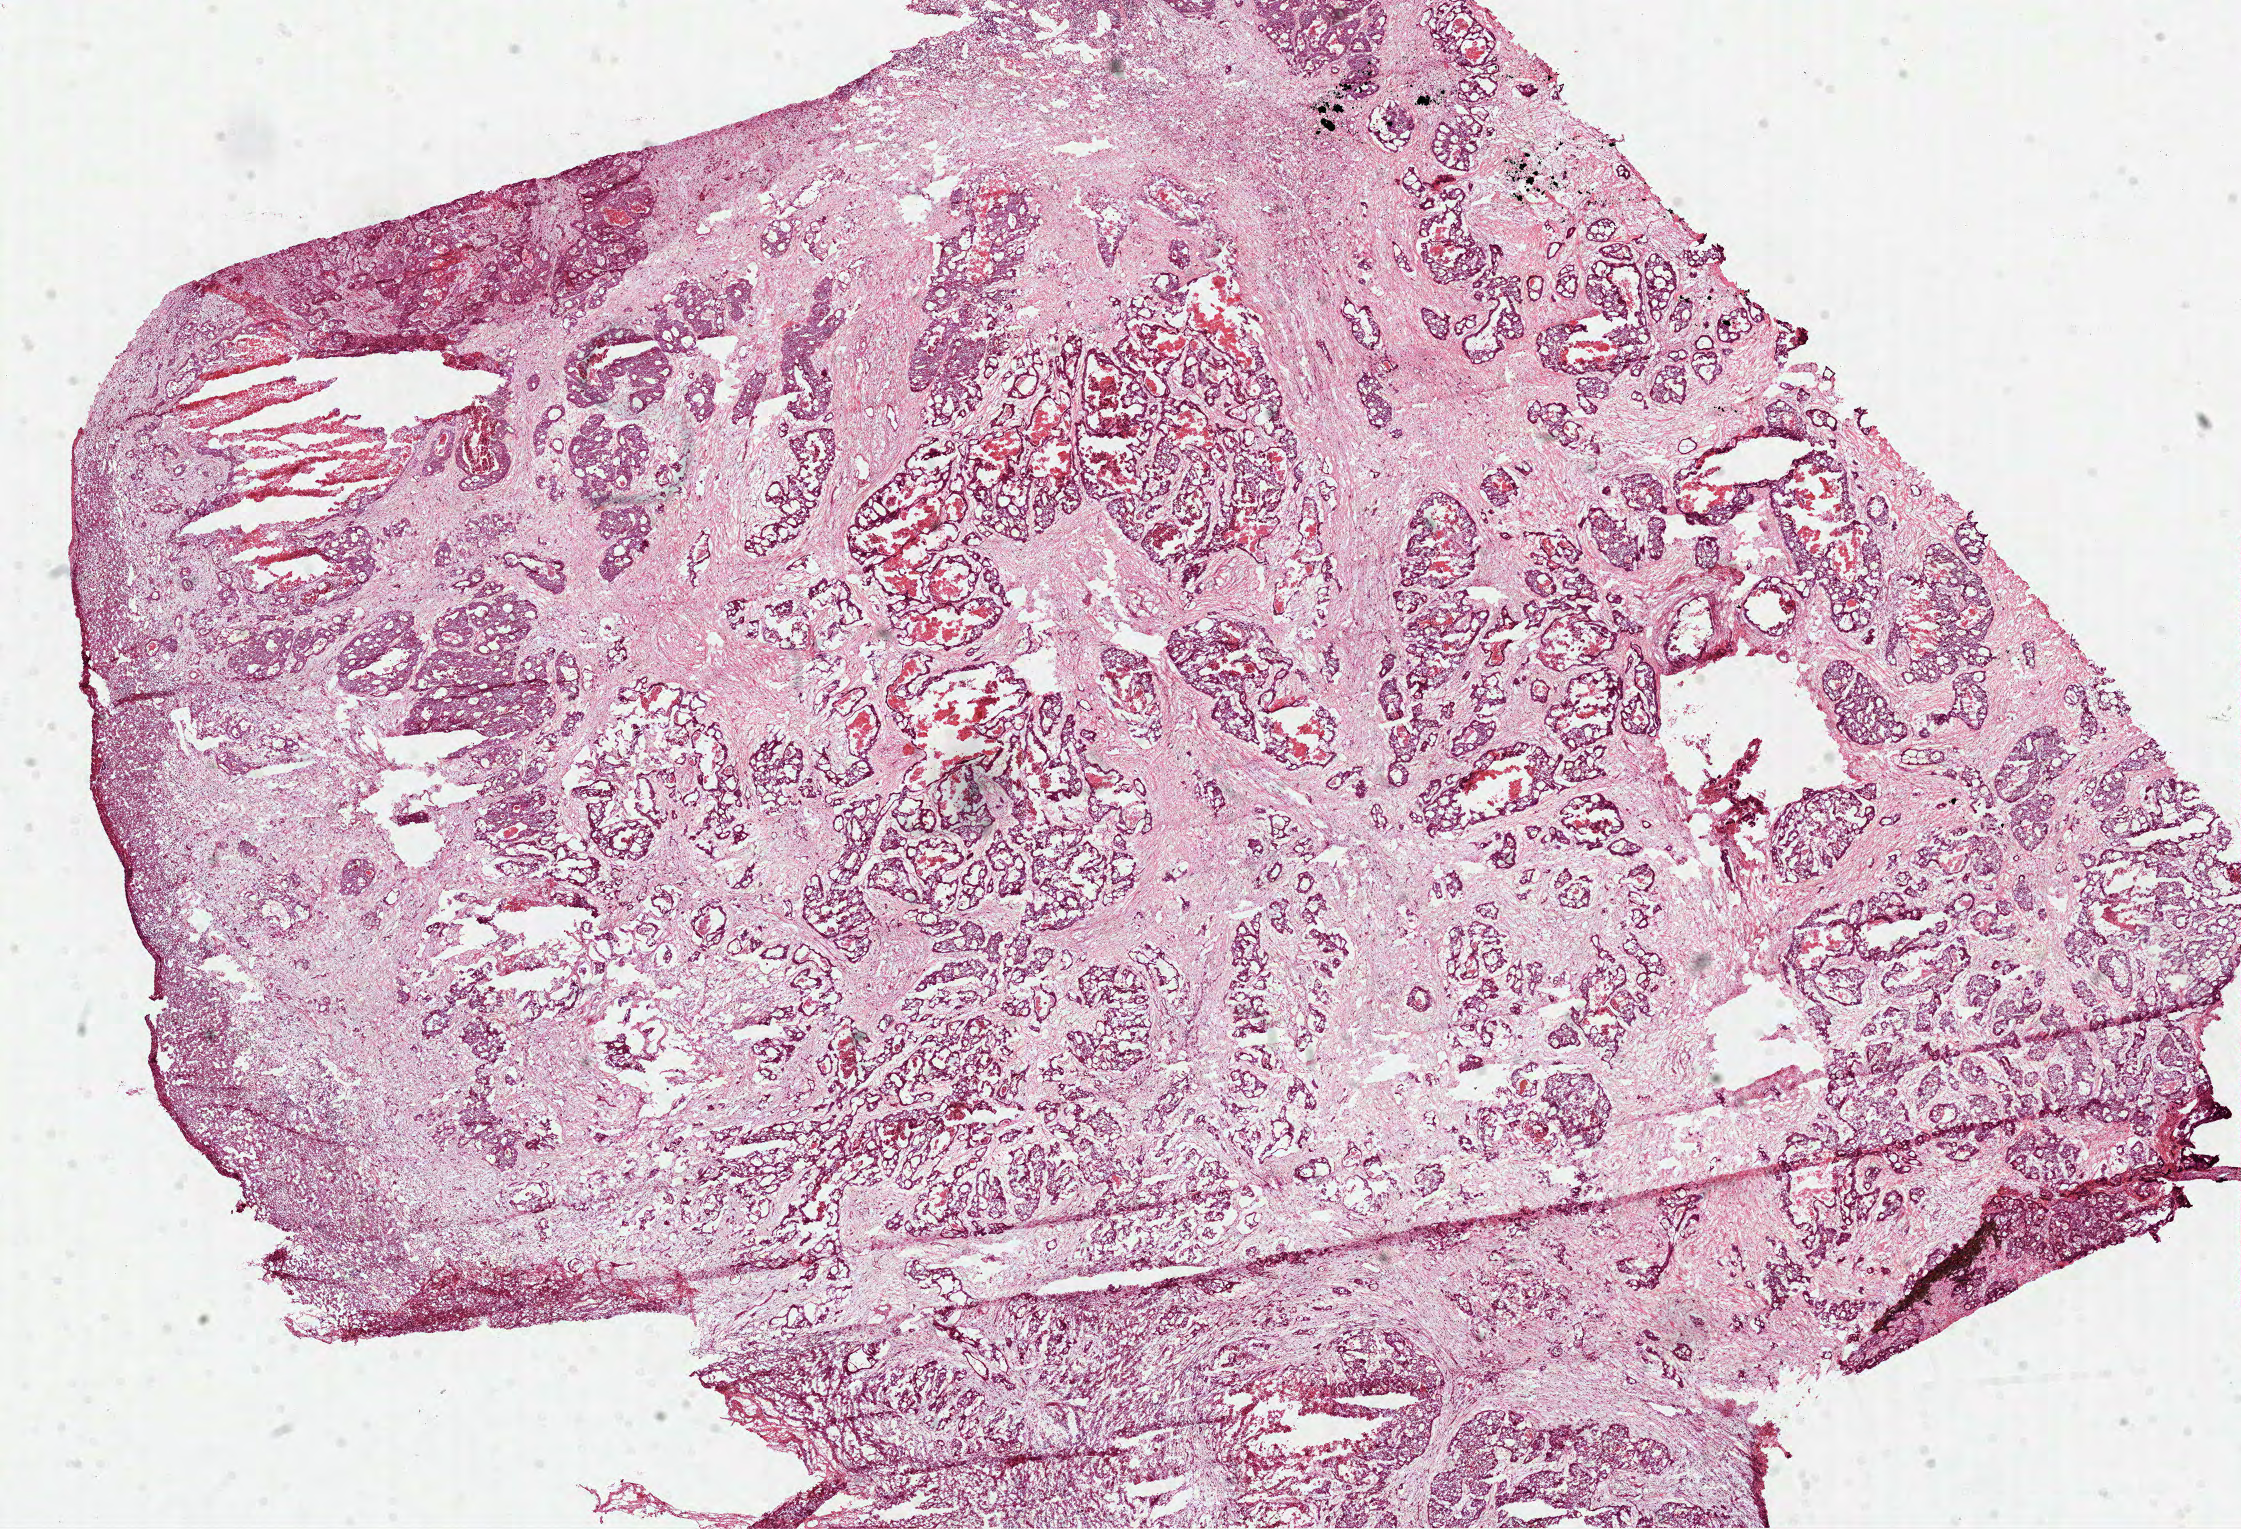
H&E-stained whole-slide image, a low-resolution overview of the entire scanned area, about 18.1 x 12.3 mm, frozen section from the top of the tissue portion, rectum, recurrent tumour sample. Male, age 56 years at initial diagnosis. Slide review estimates, as recorded: tumour cells 60%, tumour nuclei 80%, normal cells 0%, stromal cells 25%, necrosis 15%.
- this section: recurrent tumour
- patient diagnosis: Adenocarcinoma, NOS (rectosigmoid junction)